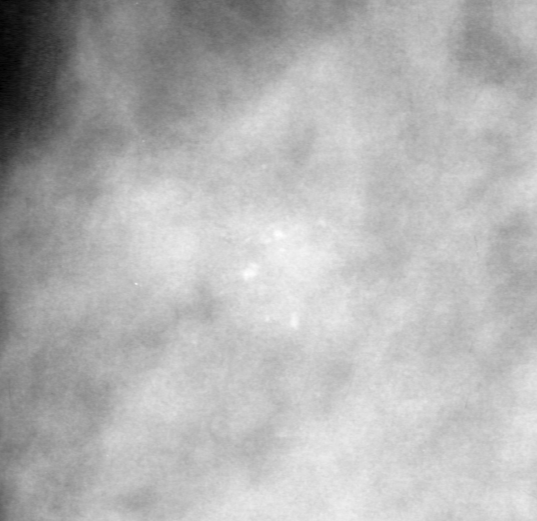
Region of interest cut from a scanned film mammogram (one marked finding); left breast; MLO view; BI-RADS breast density category 4 (scale 1–4).
- Finding: calcifications, morphology pleomorphic, distribution clustered; BI-RADS assessment category 4; pathology result (as recorded, not read from the image): malignant.